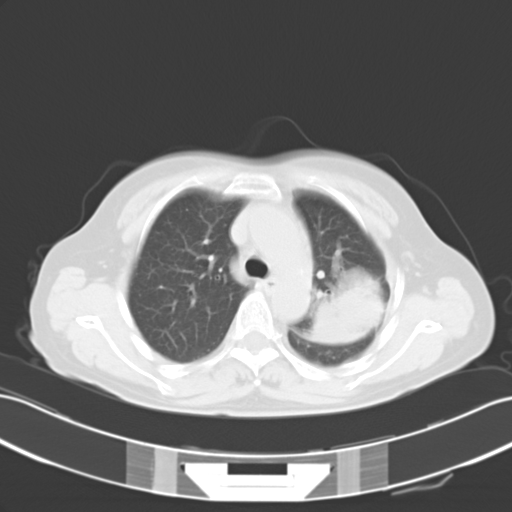
Chest CT, one axial slice. Position 18 of 25 along the scan axis. Reconstruction kernel B40f. Lung window (W 1500 / L -600 HU). 10 mm slice thickness. 512 × 512 image matrix. Female patient, age 54 years. From the clinical record (not read from this slice): clinical TNM (as recorded): T3 N1 M0.
Structures marked on this image (bounding box drawn by a radiologist):
- lung tumour (recorded histology: adenocarcinoma): bounding box <310,270,388,351> (left, top, right, bottom; pixels)